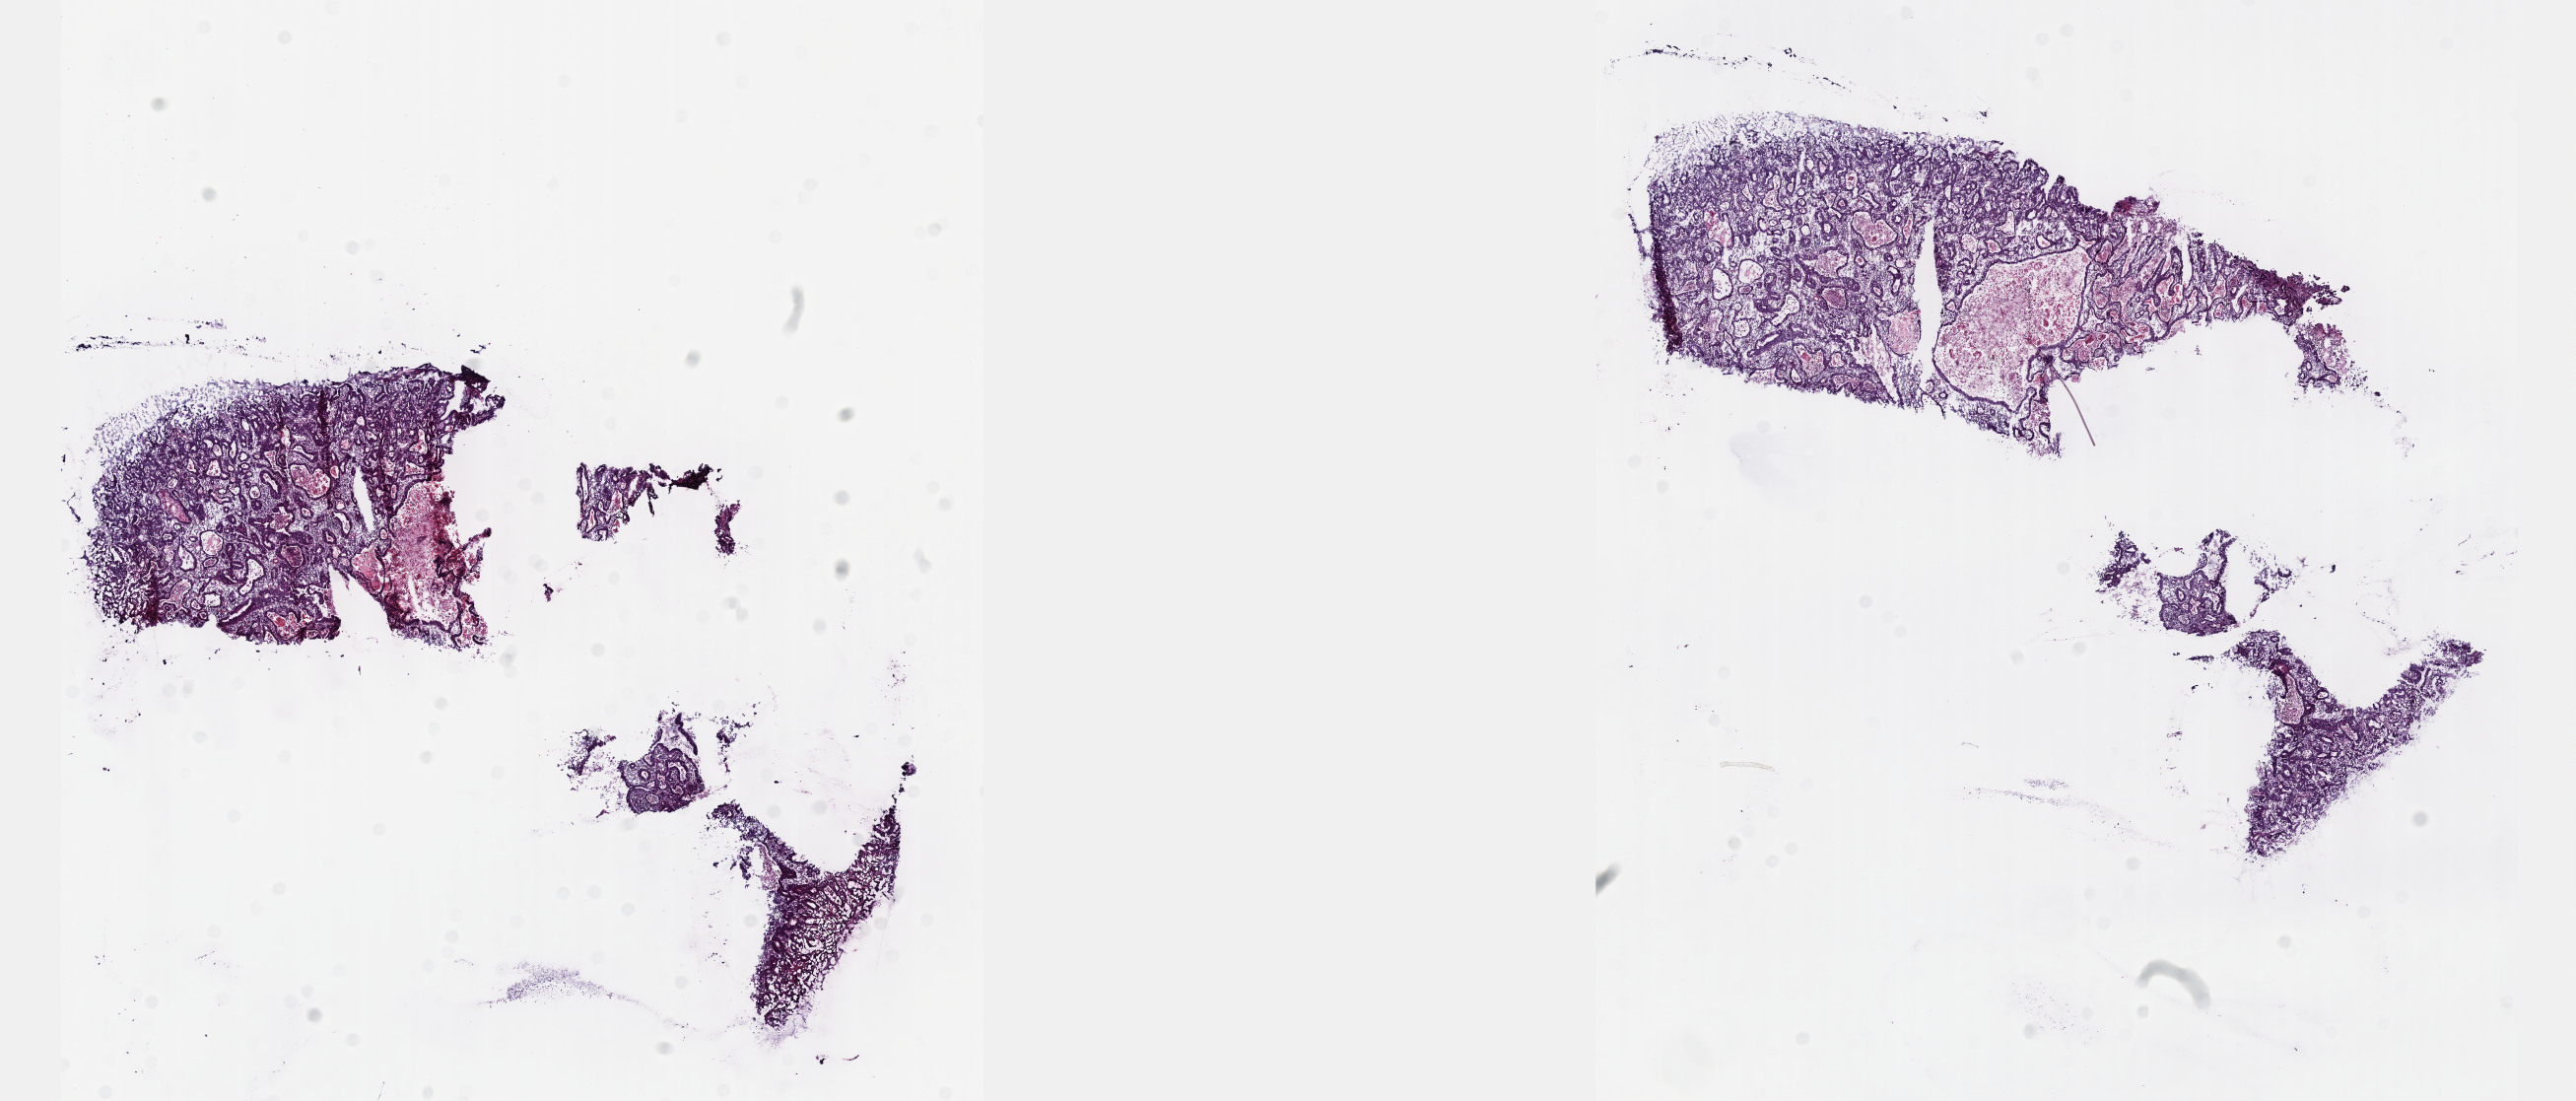
Hematoxylin and eosin (H&E) stained whole-slide image — a low-resolution overview of the entire scanned area, about 21.1 x 9.0 mm; frozen section; primary tumour sample from the stomach. Patient: male, age at initial diagnosis 51 years.
Pathologic diagnosis: Adenocarcinoma, intestinal type.